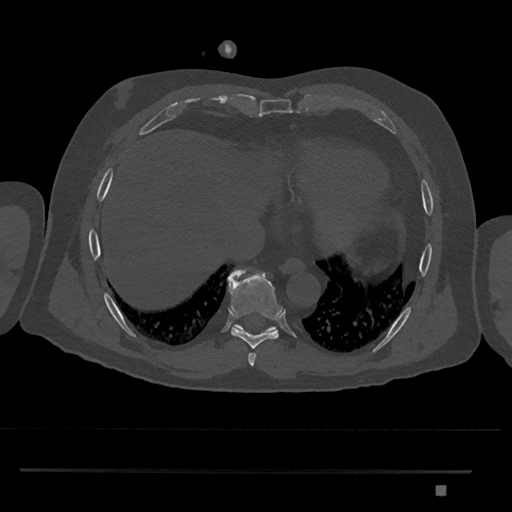
CT including the spine, one axial slice; position 1098 of 1134 along the scan axis; reconstruction kernel Br40s/3; 120 kVp; bone window (W 1800 / L 400 HU); 0.5 mm slice thickness; 512 × 512 image matrix, field of view 429 × 429 mm. Patient: male, 65 years. From the clinical record (not read from this slice): primary cancer: prostate.
Annotated regions visible in this slice (semi-automatic segmentation, software-assisted and operator-edited):
- T8 vertebra: bounding box <228,269,284,348> (left, top, right, bottom; pixels)
- T9 vertebra: <233,324,277,332>